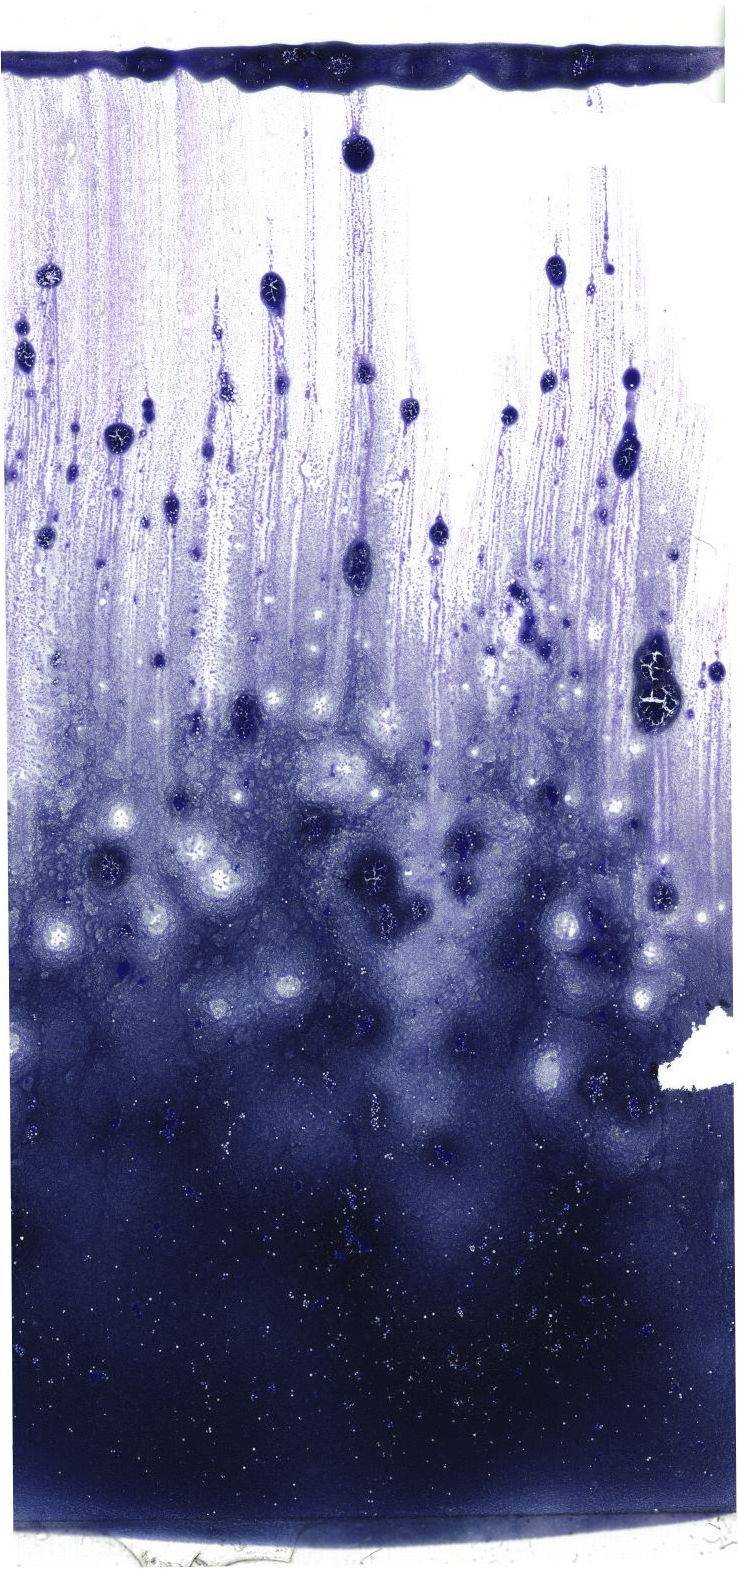
May-Grünwald–Giemsa-stained marrow aspirate smear (whole slide), whole scanned area (about 20.9 x 44.5 mm) shown as a low-resolution overview. Patient sex: male.
Diagnosis: Chronic Phase Chronic Myeloid Leukemia, BCR-ABL1 Positive.